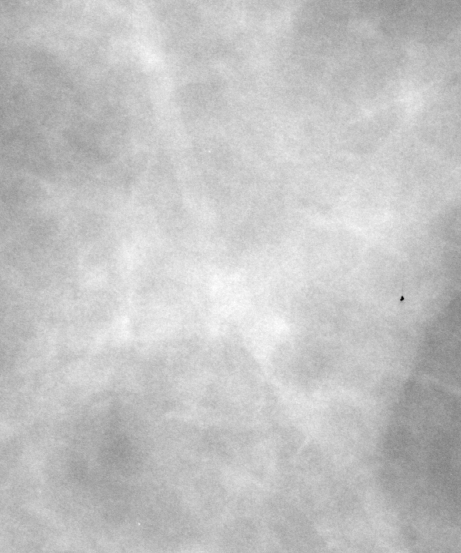
Cropped region of a digitized screen-film mammogram centred on a radiologist-marked abnormality; right breast; CC view.
Mass, shape asymmetric breast tissue, margins ill defined; BI-RADS assessment category 3; subtlety rating 5 on a 1 (subtle) to 5 (obvious) scale; benign; no additional work-up was recommended (benign without callback).